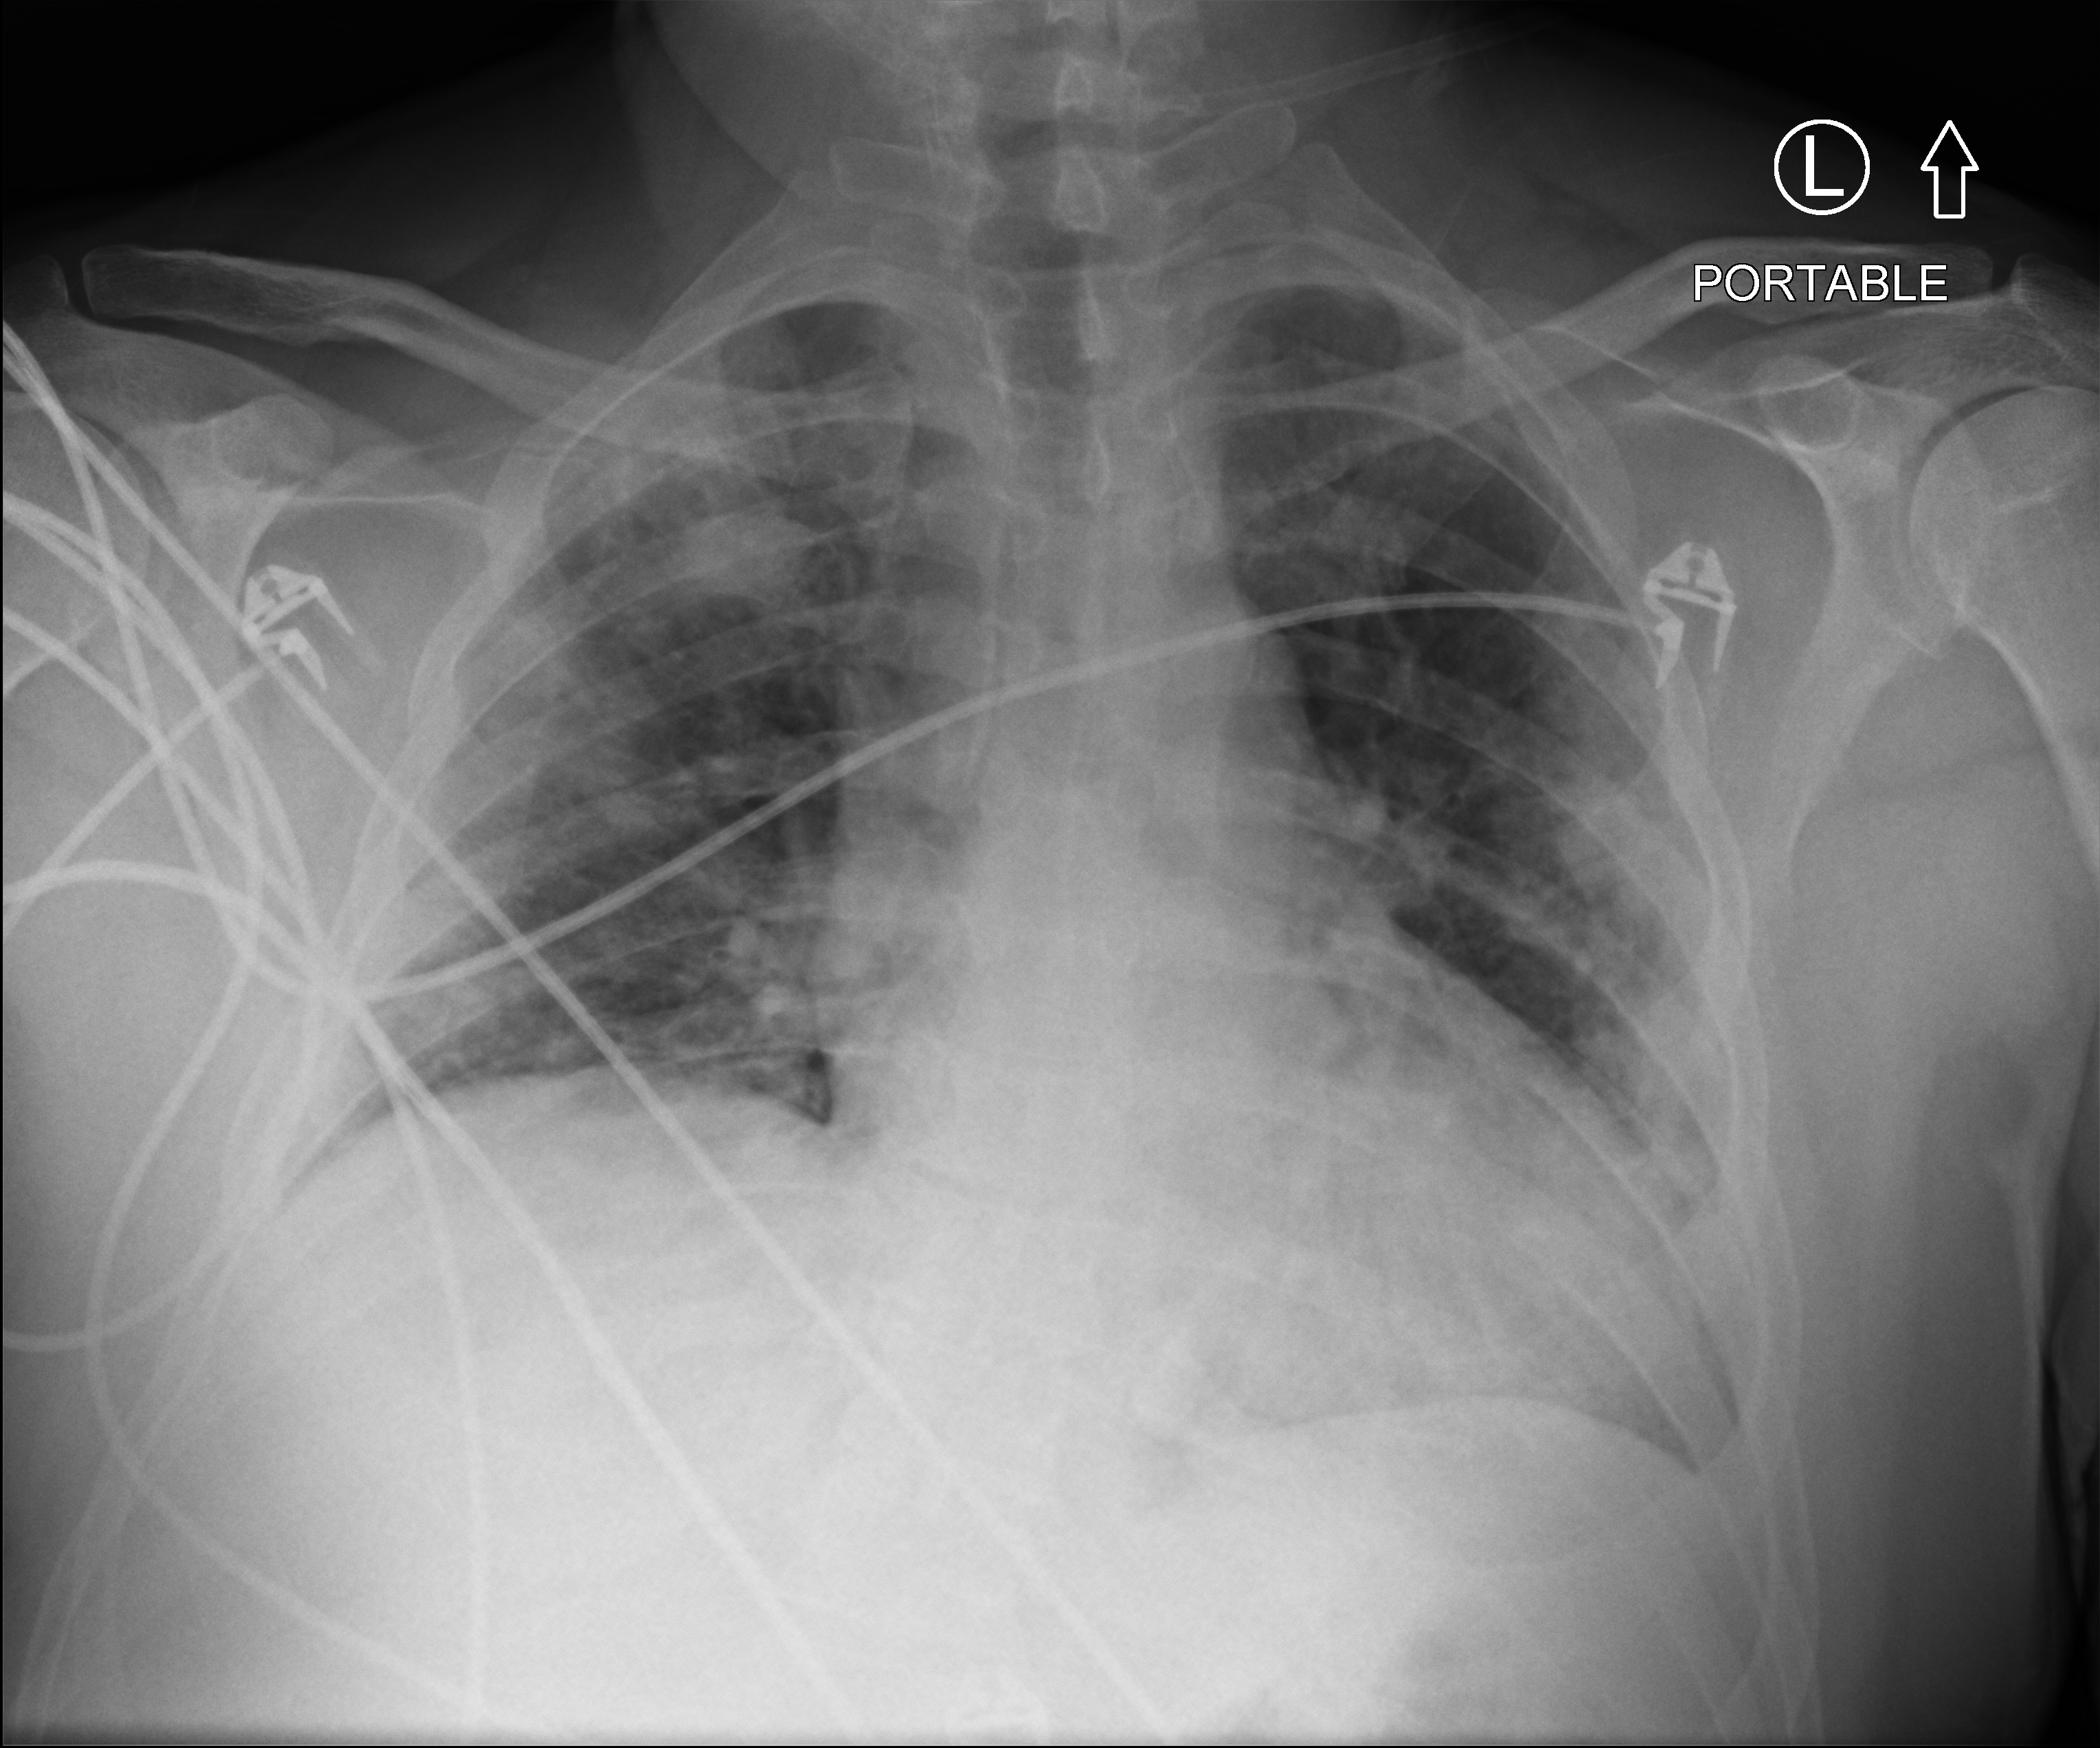
Portable chest radiograph. Patient hospitalised with COVID-19; male, aged 18–59 years.
Admission-level facts for this patient (not findings on this image; timing relative to this image not recorded):
- length of hospital stay: 32 days
- admitted to intensive care during this hospital stay: no
- mechanically ventilated during this hospital stay: yes